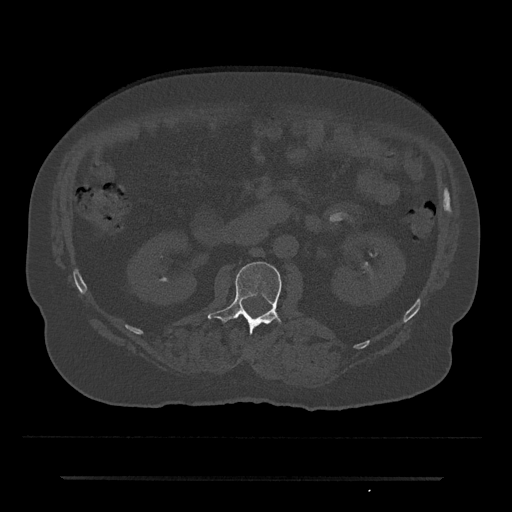
CT including the spine, one axial slice. Position 15 of 797 along the scan axis. Reconstruction kernel Br40s/3. 120 kVp. Bone window (W 1800 / L 400 HU). 0.5 mm slice thickness. 512 × 512 image matrix, field of view 437 × 437 mm. Male patient, age 69 years. Case-level facts recorded for this patient, not image findings: primary cancer: prostate.
Annotated regions visible in this slice (semi-automatically segmented with operator editing):
- L2 vertebra: bounding box (x1, y1, x2, y2) in pixels: (208, 261, 282, 333)